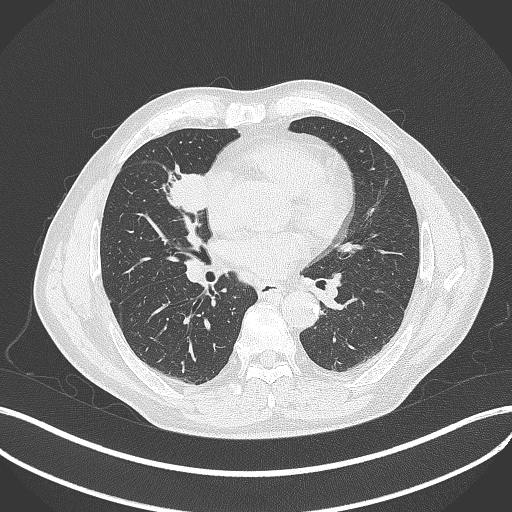
Chest CT, one axial slice; slice 193 of 429 in the series (ordered by position); 120 kVp; lung window (W 1500 / L -600 HU); 1 mm slice thickness; 512 × 512 image matrix, field of view 400 × 400 mm. Male patient, age 61 years. From the clinical record (not read from this slice): clinical TNM (as recorded): T2b N1 M0.
Annotated regions visible in this slice (rectangle marked by the reading radiologist):
- lung tumour (recorded histology: squamous cell carcinoma): bounding box <161,159,209,218> (left, top, right, bottom; pixels)